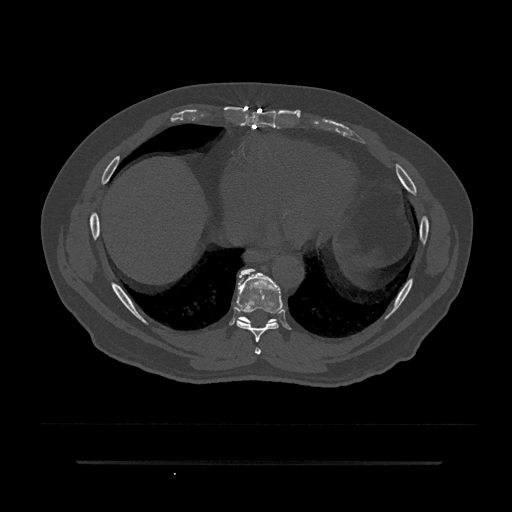
CT including the spine, one axial slice. Position 413 of 797 along the scan axis. 120 kVp. Bone window (W 1800 / L 400 HU). 512 × 512 image matrix, field of view 464 × 464 mm. Patient: male, 59 years. Case-level facts recorded for this patient, not image findings: primary cancer: bile ducts; vertebrae with lytic lesions (as recorded): T10.
Annotated regions visible in this slice (semi-automatic segmentation, software-assisted and operator-edited):
- T7 vertebra: bounding box [x1, y1, x2, y2] px = [255, 347, 261, 355]
- T8 vertebra: [236, 269, 283, 343]
- T9 vertebra: [237, 273, 276, 323]